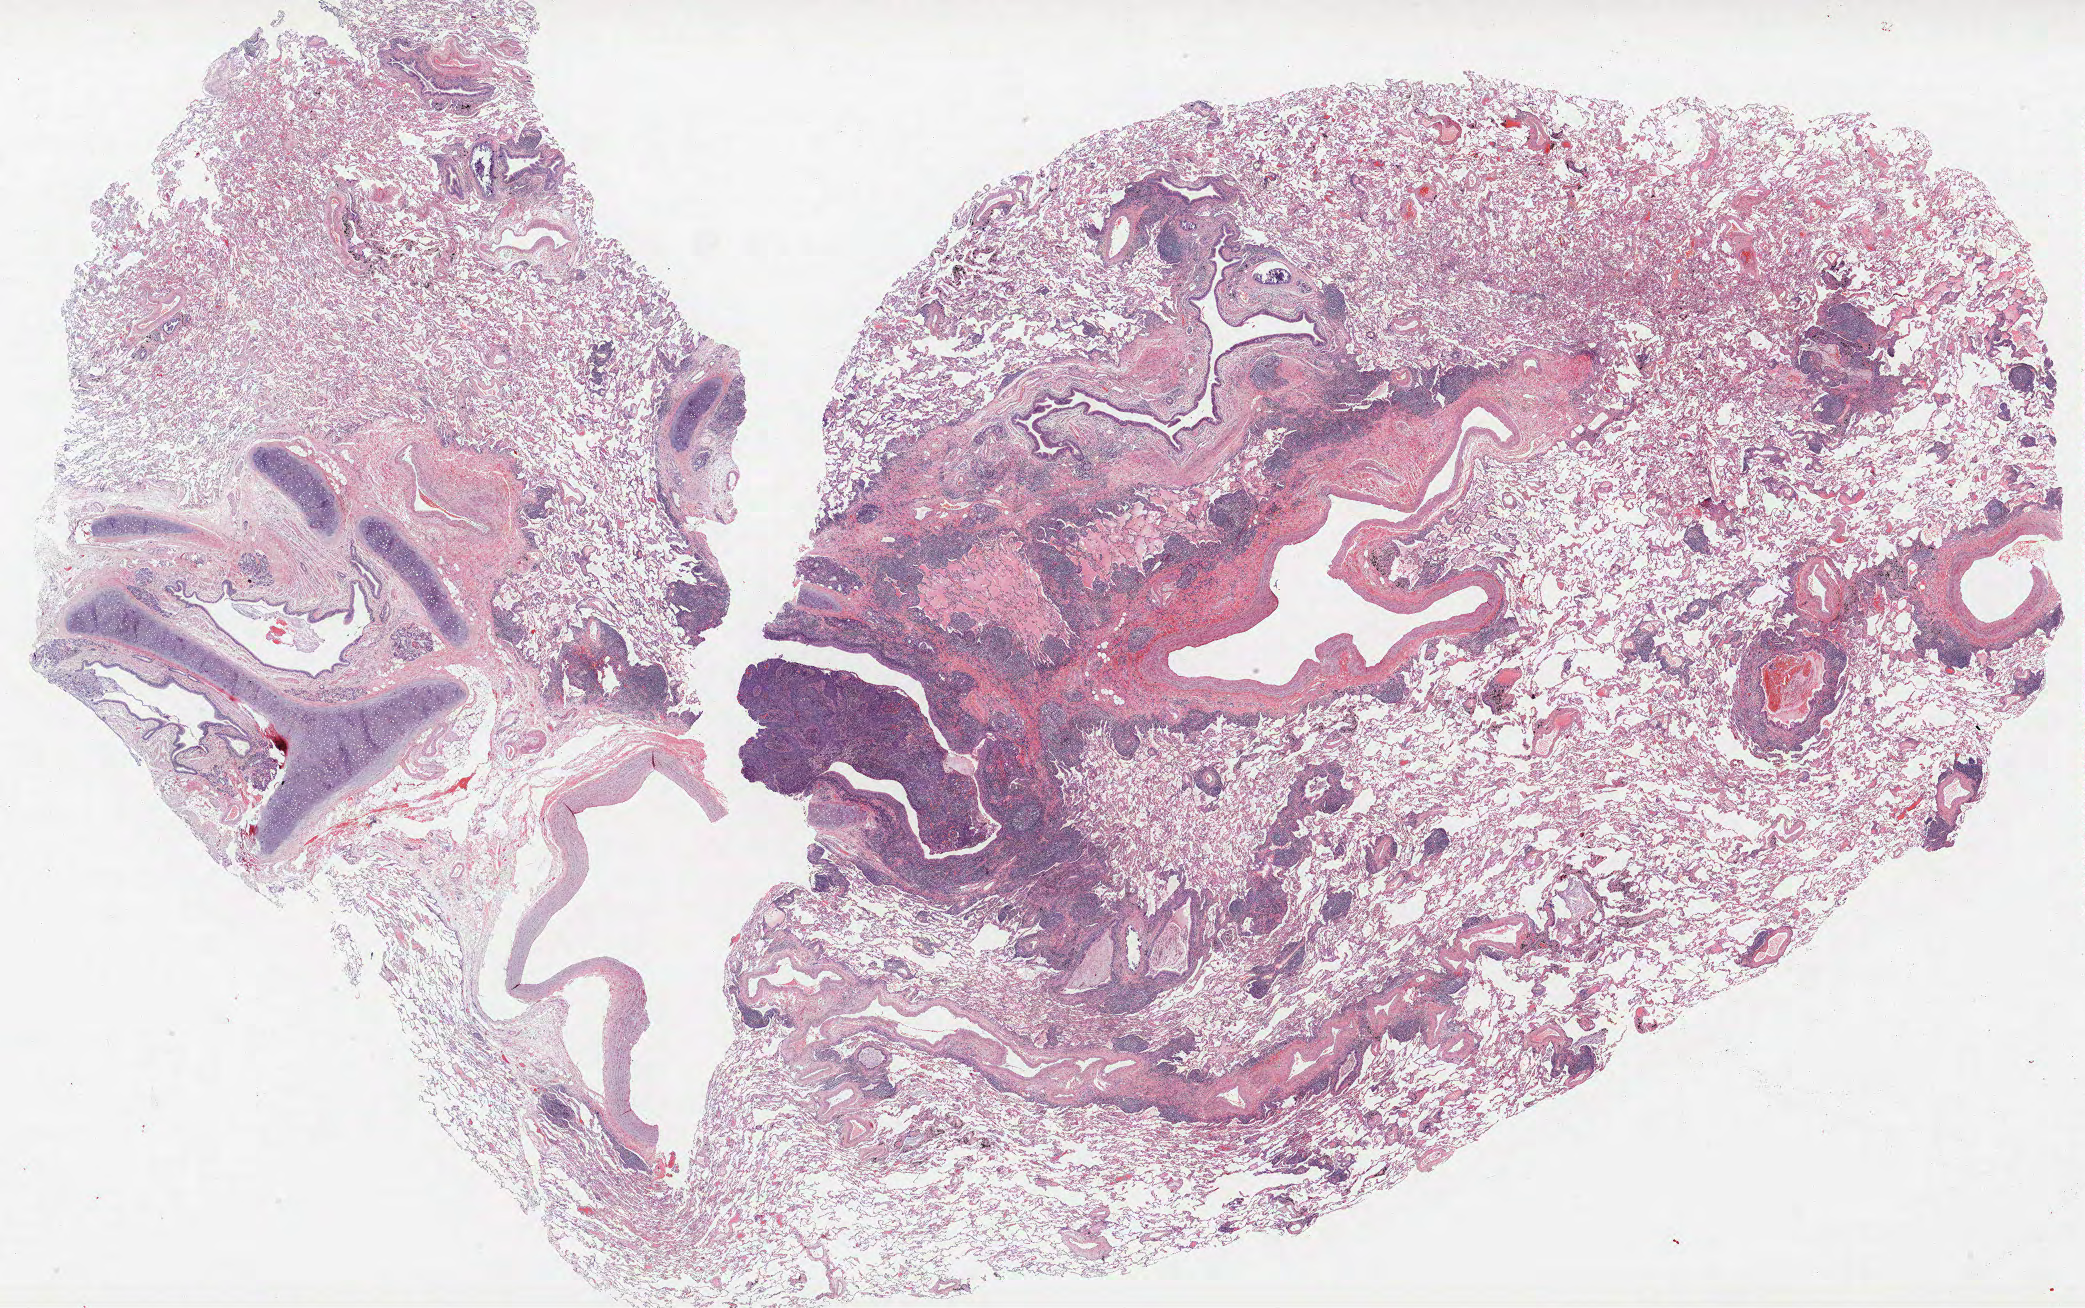
Whole-slide histology image, H&E, shown as a low-resolution overview of the whole scanned area (about 33.4 x 20.9 mm, acquisition: 40x scan), formalin-fixed paraffin-embedded (FFPE) section, lung. Male, age 73 at enrolment. Former smoker at enrolment.
Stage (AJCC 6th edition): IA. Primary tumour location (clinical record): right lower lobe. Tumour size (pathology): 30 mm. Participant's lung-cancer diagnosis: Non-small cell carcinoma.